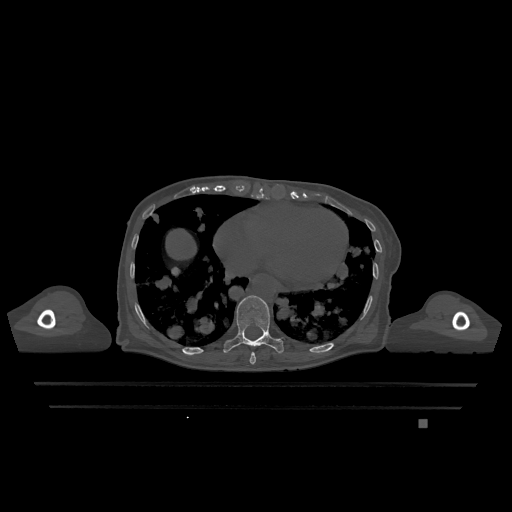
CT including the spine, one axial slice; position 648 of 1317 along the scan axis; bone window (W 1800 / L 400 HU); 0.5 mm slice thickness; 512 × 512 image matrix, field of view 500 × 500 mm. Patient: female, 74 years. From the clinical record (not read from this slice): primary cancer: lung.
Outlined on this slice (semi-automatically segmented with operator editing):
- T10 vertebra: bounding box [x1, y1, x2, y2] px = [223, 295, 284, 354]
- T9 vertebra: [249, 352, 256, 365]